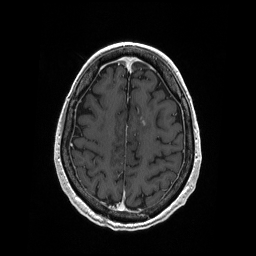
Brain MRI from a brain-tumour surgery series, one axial slice. Slice 65 of 208 in the series (ordered by position). T1-weighted post-contrast. 1 mm slice thickness. 256 × 256 image matrix. From the clinical record (not read from this slice): histopathology: Primary diffuse large B-cell lymphoma; tumour location: Left Corpus Callosum (Frontal).
Outlined on this slice (outlined manually by an expert reader):
- tumour: bounding box (x1, y1, x2, y2) in pixels: (142, 120, 146, 127)